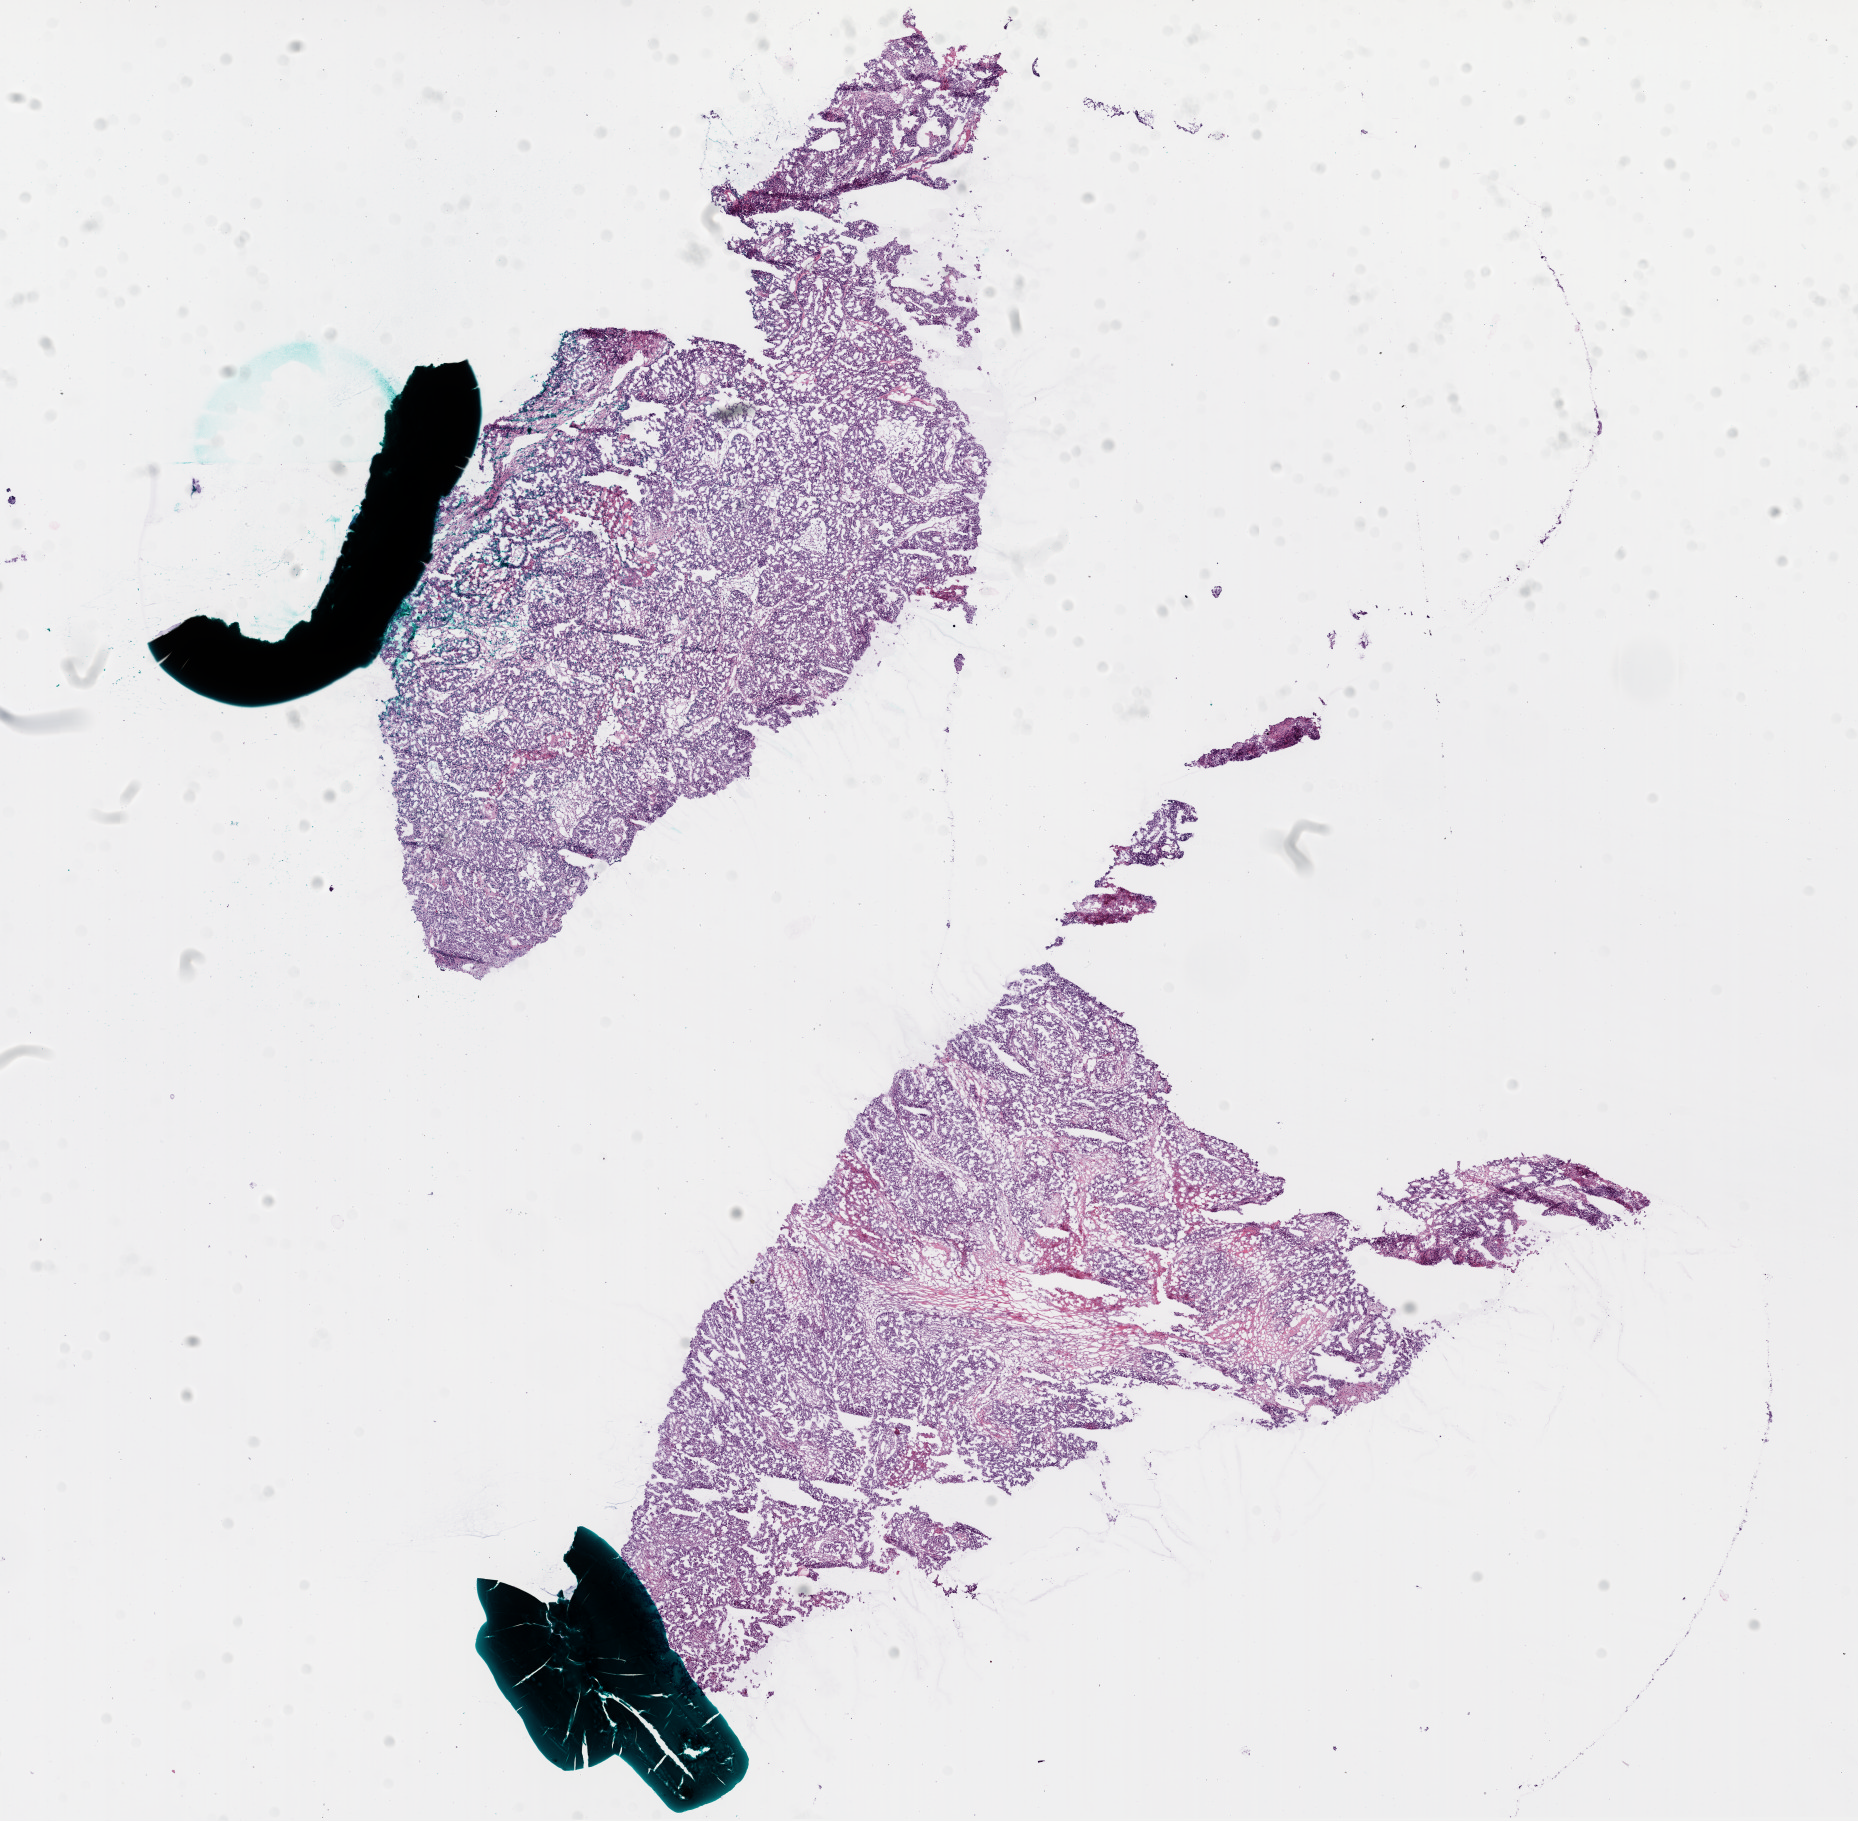
Hematoxylin and eosin (H&E) stained whole-slide image, a low-resolution overview of the entire scanned area, about 15.0 x 14.7 mm (slide scanned at 20x); frozen section; primary tumour sample from the ovary. Female, age 62 years at initial diagnosis. Histologic grade: G3 (poorly differentiated). Composition of this section per pathologist review: tumour cells 85%, tumour nuclei 95%, normal cells 0%, stromal cells 10%, necrosis 5%.
• histologic diagnosis: Serous cystadenocarcinoma, NOS
• laterality: bilateral
• FIGO stage: IIC